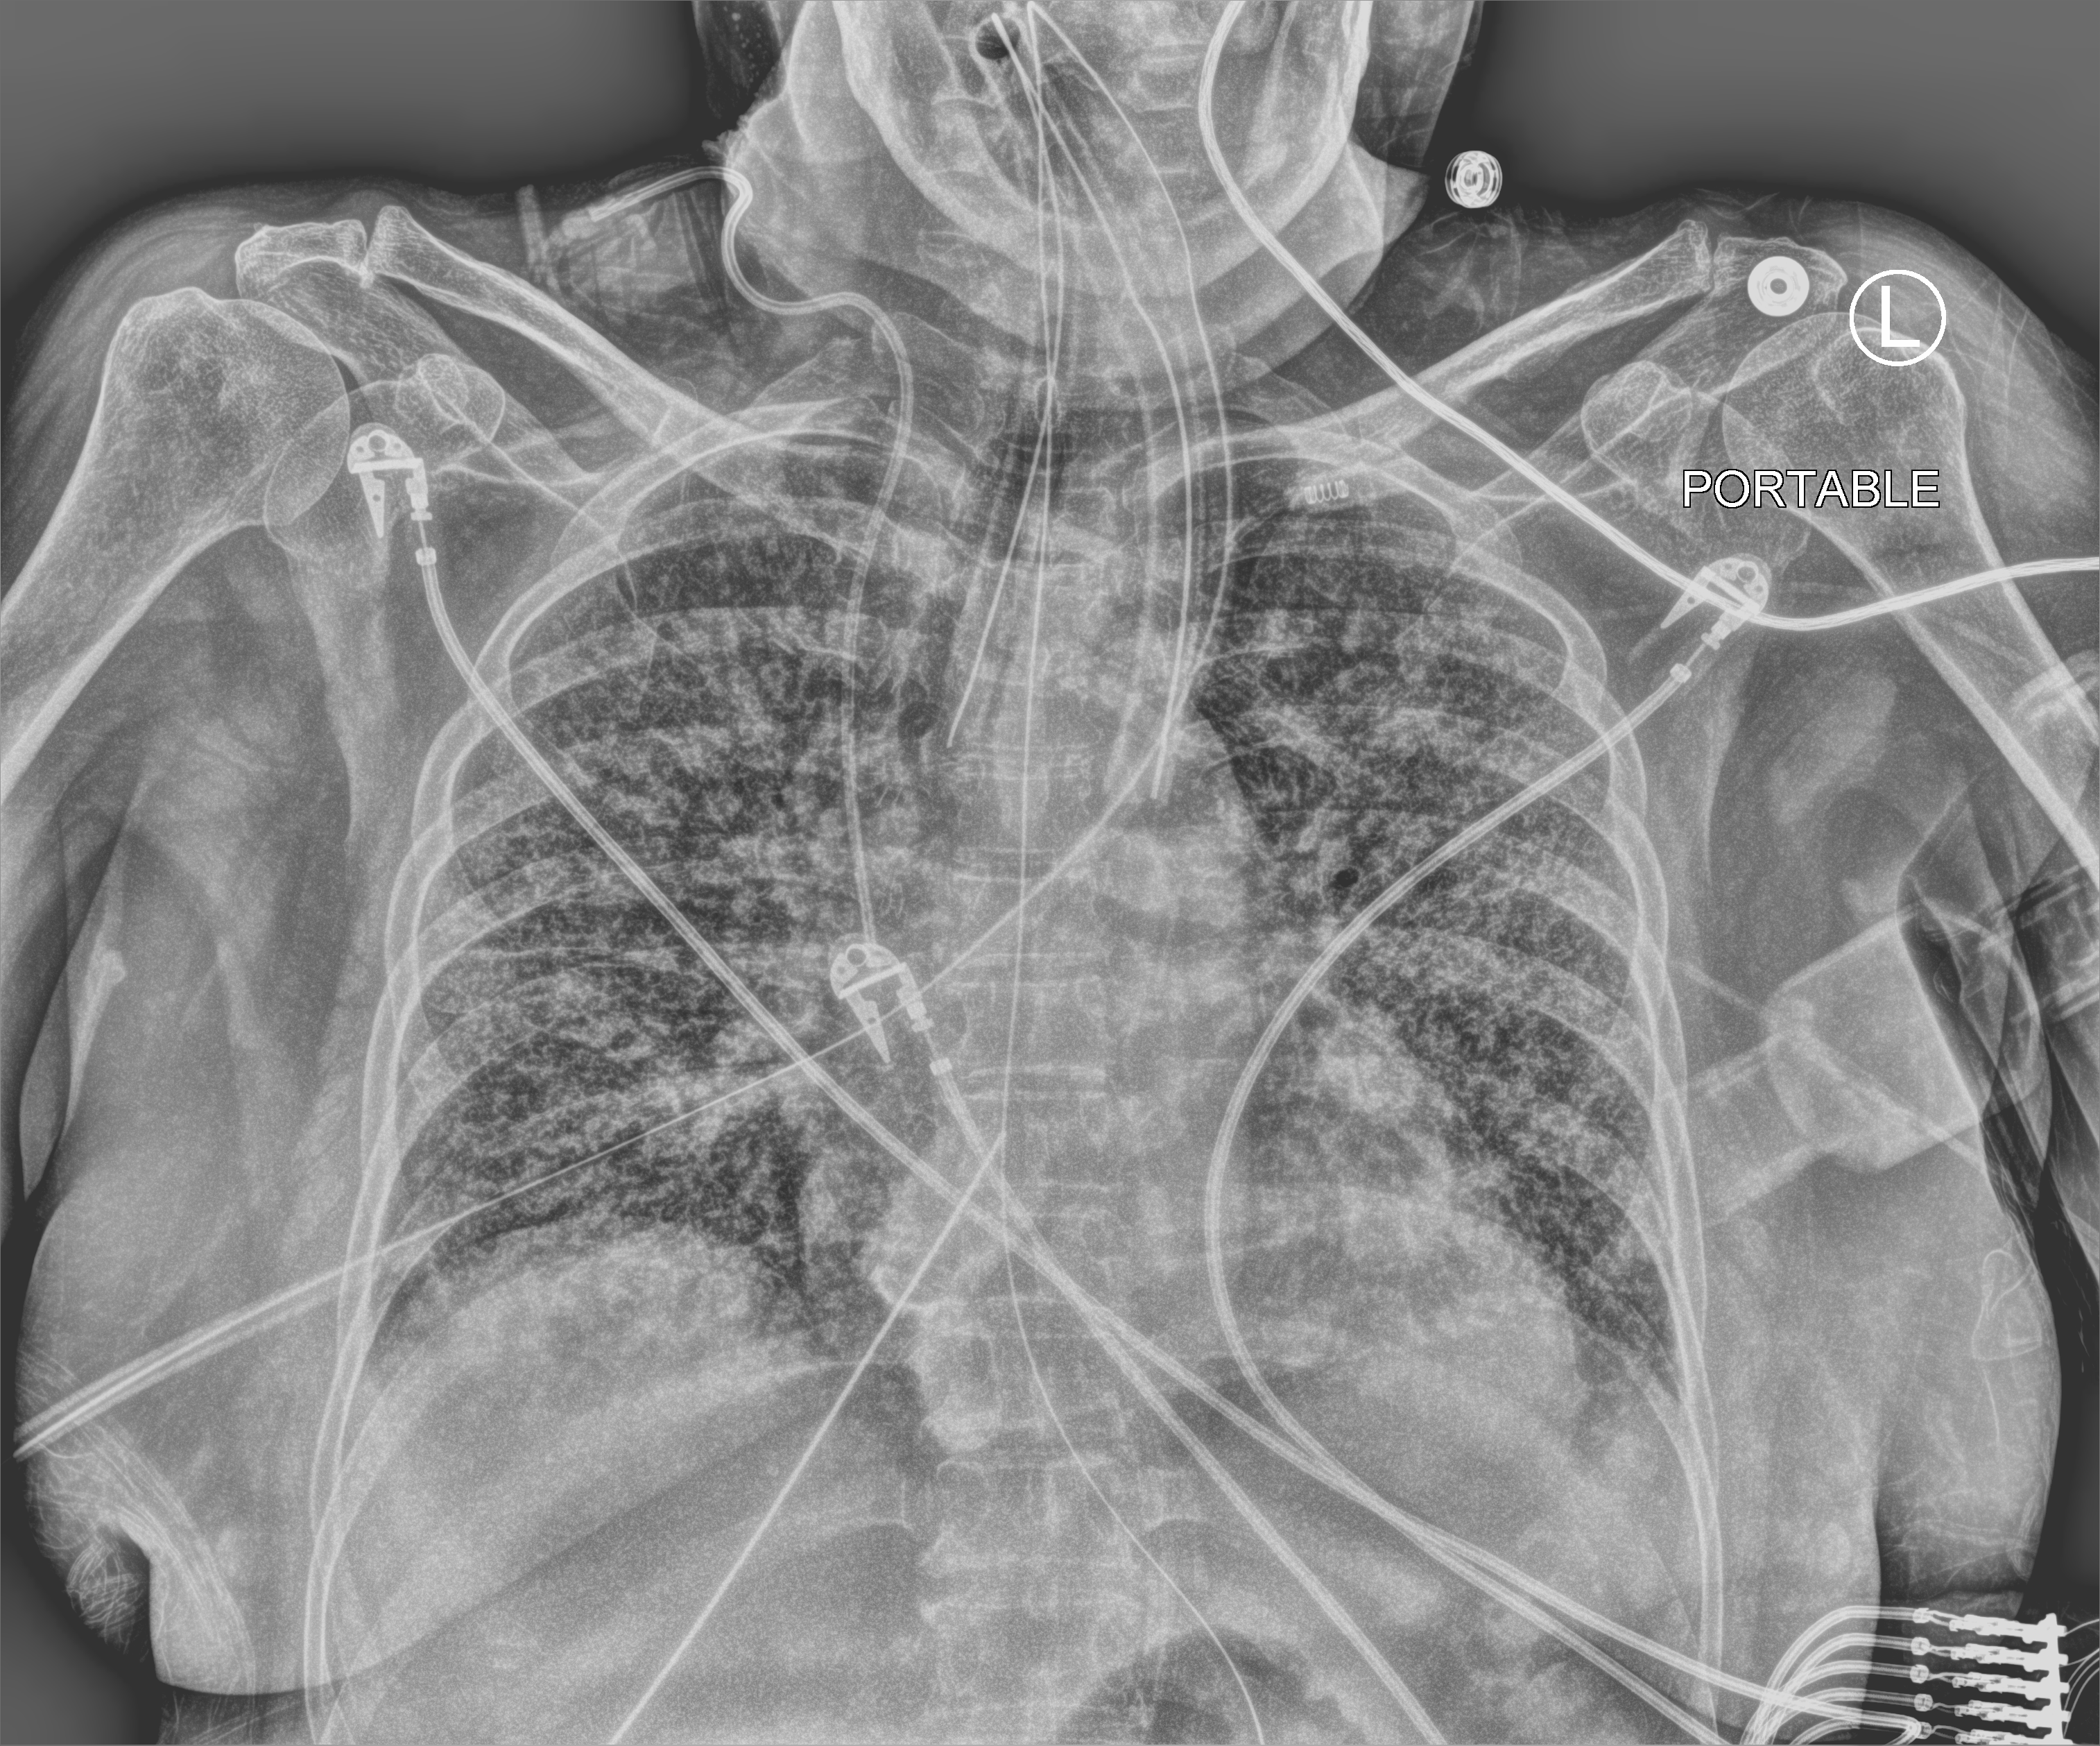
Bedside chest radiograph (computed radiography); anteroposterior (AP) projection. Female patient hospitalised with COVID-19, age 60–74 years.
Admission-level facts for this patient (not findings on this image; timing relative to this image not recorded): mechanically ventilated during this hospital stay: yes.